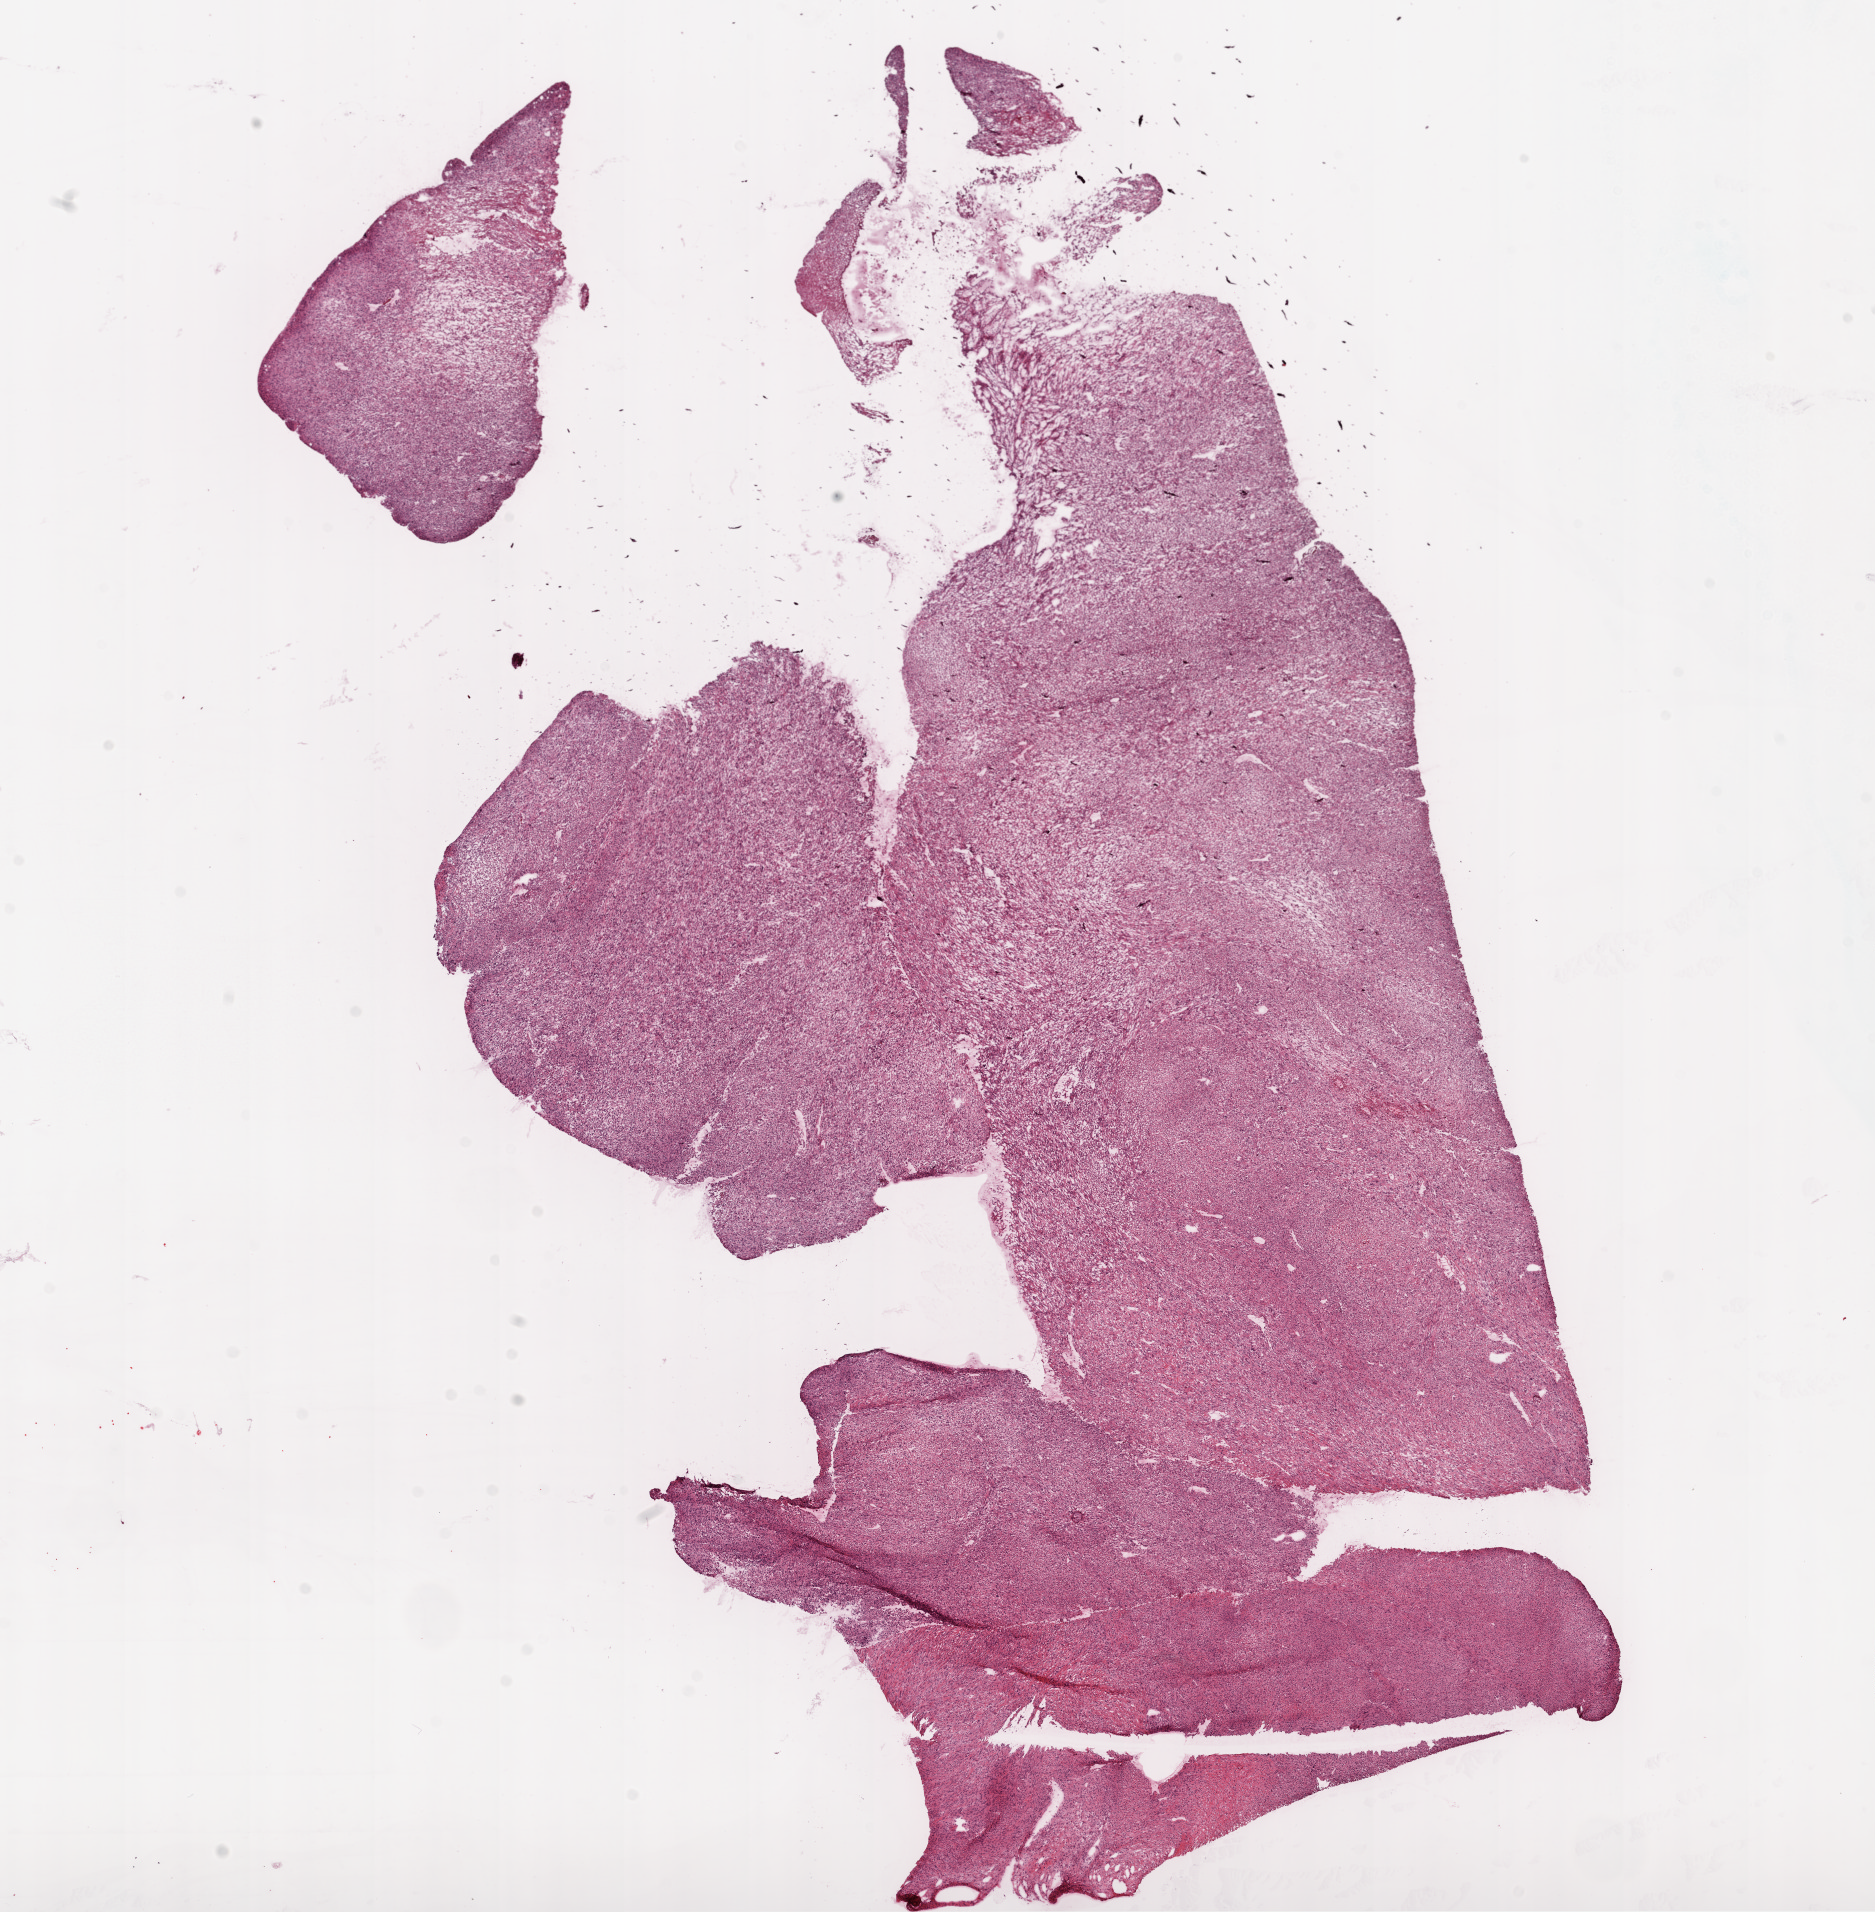
Whole-slide histology image, H&E, whole scanned area (about 15.0 x 15.3 mm) shown as a low-resolution overview. Frozen section from the top of the tissue portion. Primary tumour sample from the kidney. Patient: female, age at initial diagnosis 73 years. Histologic grade: G4 (undifferentiated). Pathologist review of this section (percent, as recorded): tumour cells 100%, tumour nuclei 95%, normal cells 0%, stromal cells 0%, necrosis 0%. Infiltration values recorded for this section: lymphocyte infiltration 1%, monocyte infiltration 0%, neutrophil infiltration 0%.
Lymph nodes positive (case pathology): 0 of 13 examined. Laterality: left. AJCC pathologic stage: IV. Diagnosis: Clear cell adenocarcinoma, NOS.